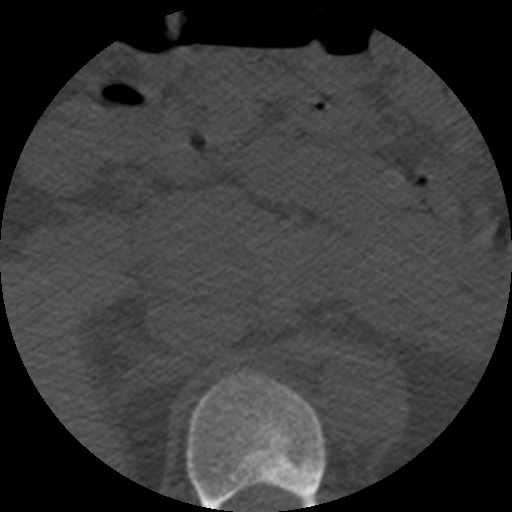
CT including the spine, one axial slice; slice 236 of 508 in the series (ordered by position); reconstruction kernel STANDARD; 120 kVp; bone window (W 1800 / L 400 HU); 1.25 mm slice thickness; 512 × 512 image matrix. Patient age 57 years. Case-level facts recorded for this patient, not image findings: primary cancer: prostate.
Structures marked on this image (semi-automatically segmented with operator editing):
- T11 vertebra: box from (x=186, y=372) to (x=326, y=512) px